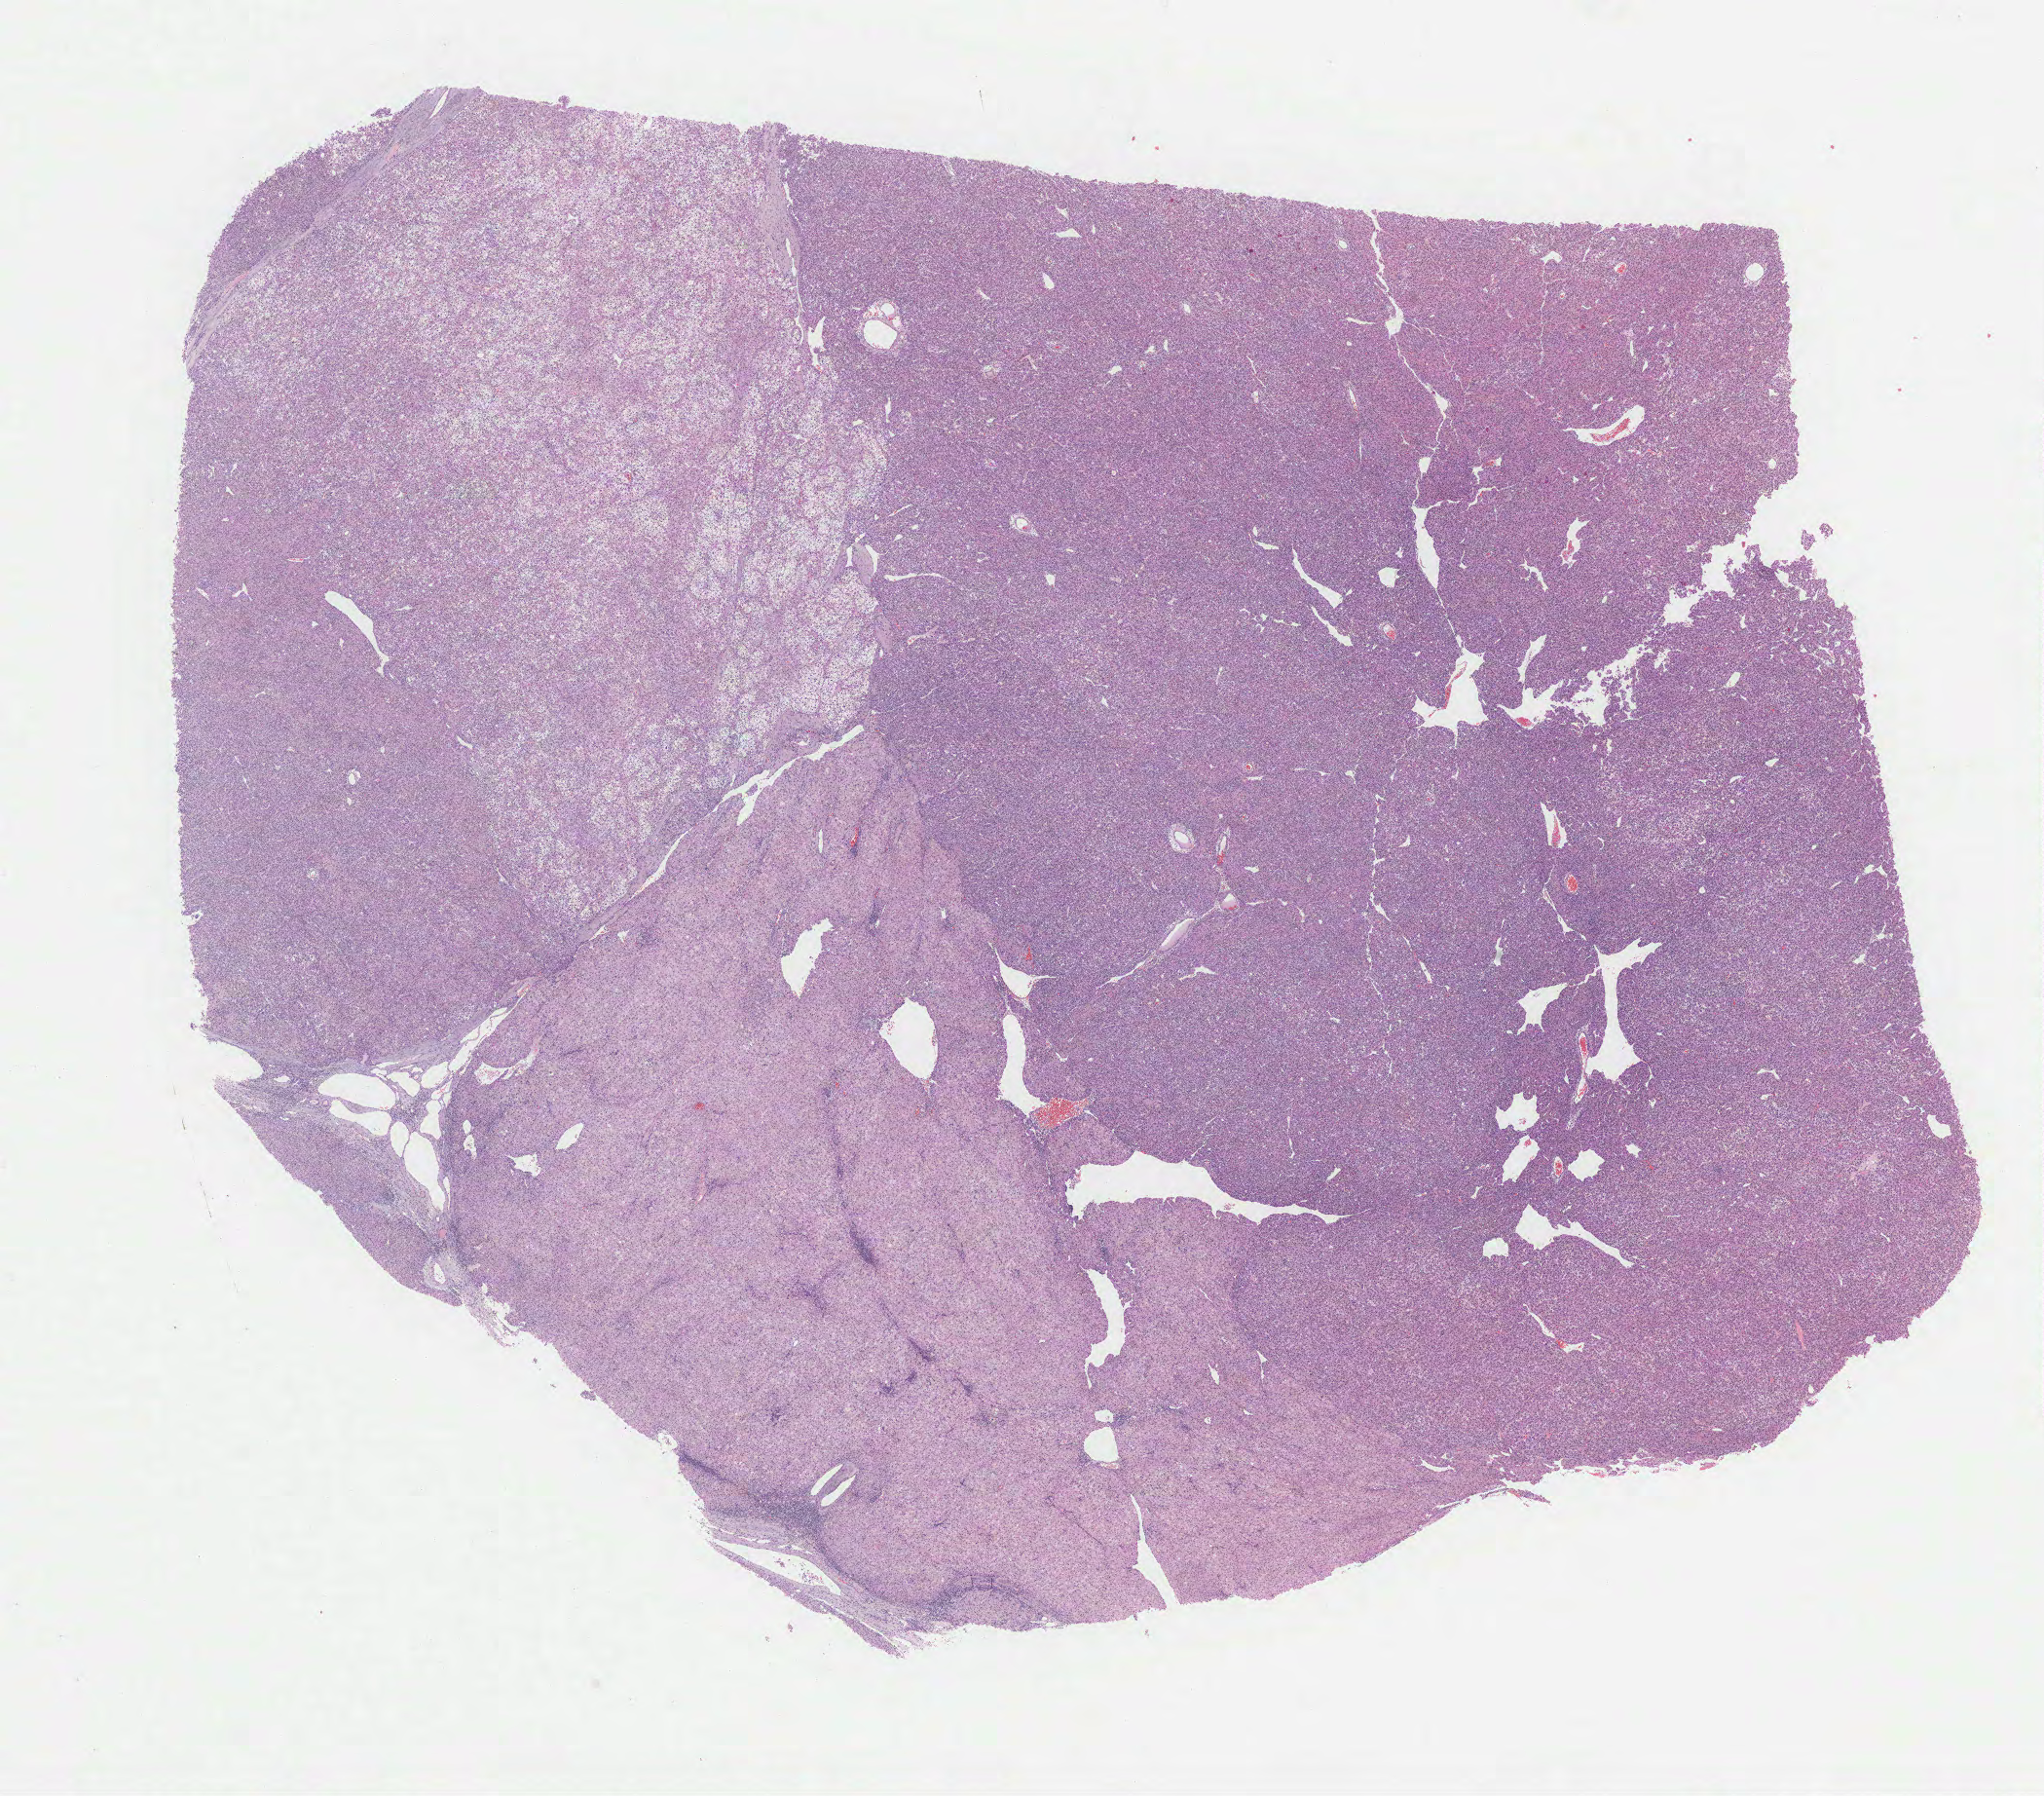
H&E whole-slide image, whole scanned area (about 17.0 x 14.9 mm, from a 40x scan) shown as a low-resolution overview, formalin-fixed paraffin-embedded (FFPE) diagnostic section, sample: primary tumour, liver. Male patient; age at initial diagnosis 51 years. Histologic grade: G2 (moderately differentiated).
• diagnosis: Hepatocellular carcinoma, NOS
• AJCC pathologic stage: I (6th edition)
• TNM: T1 NX MX